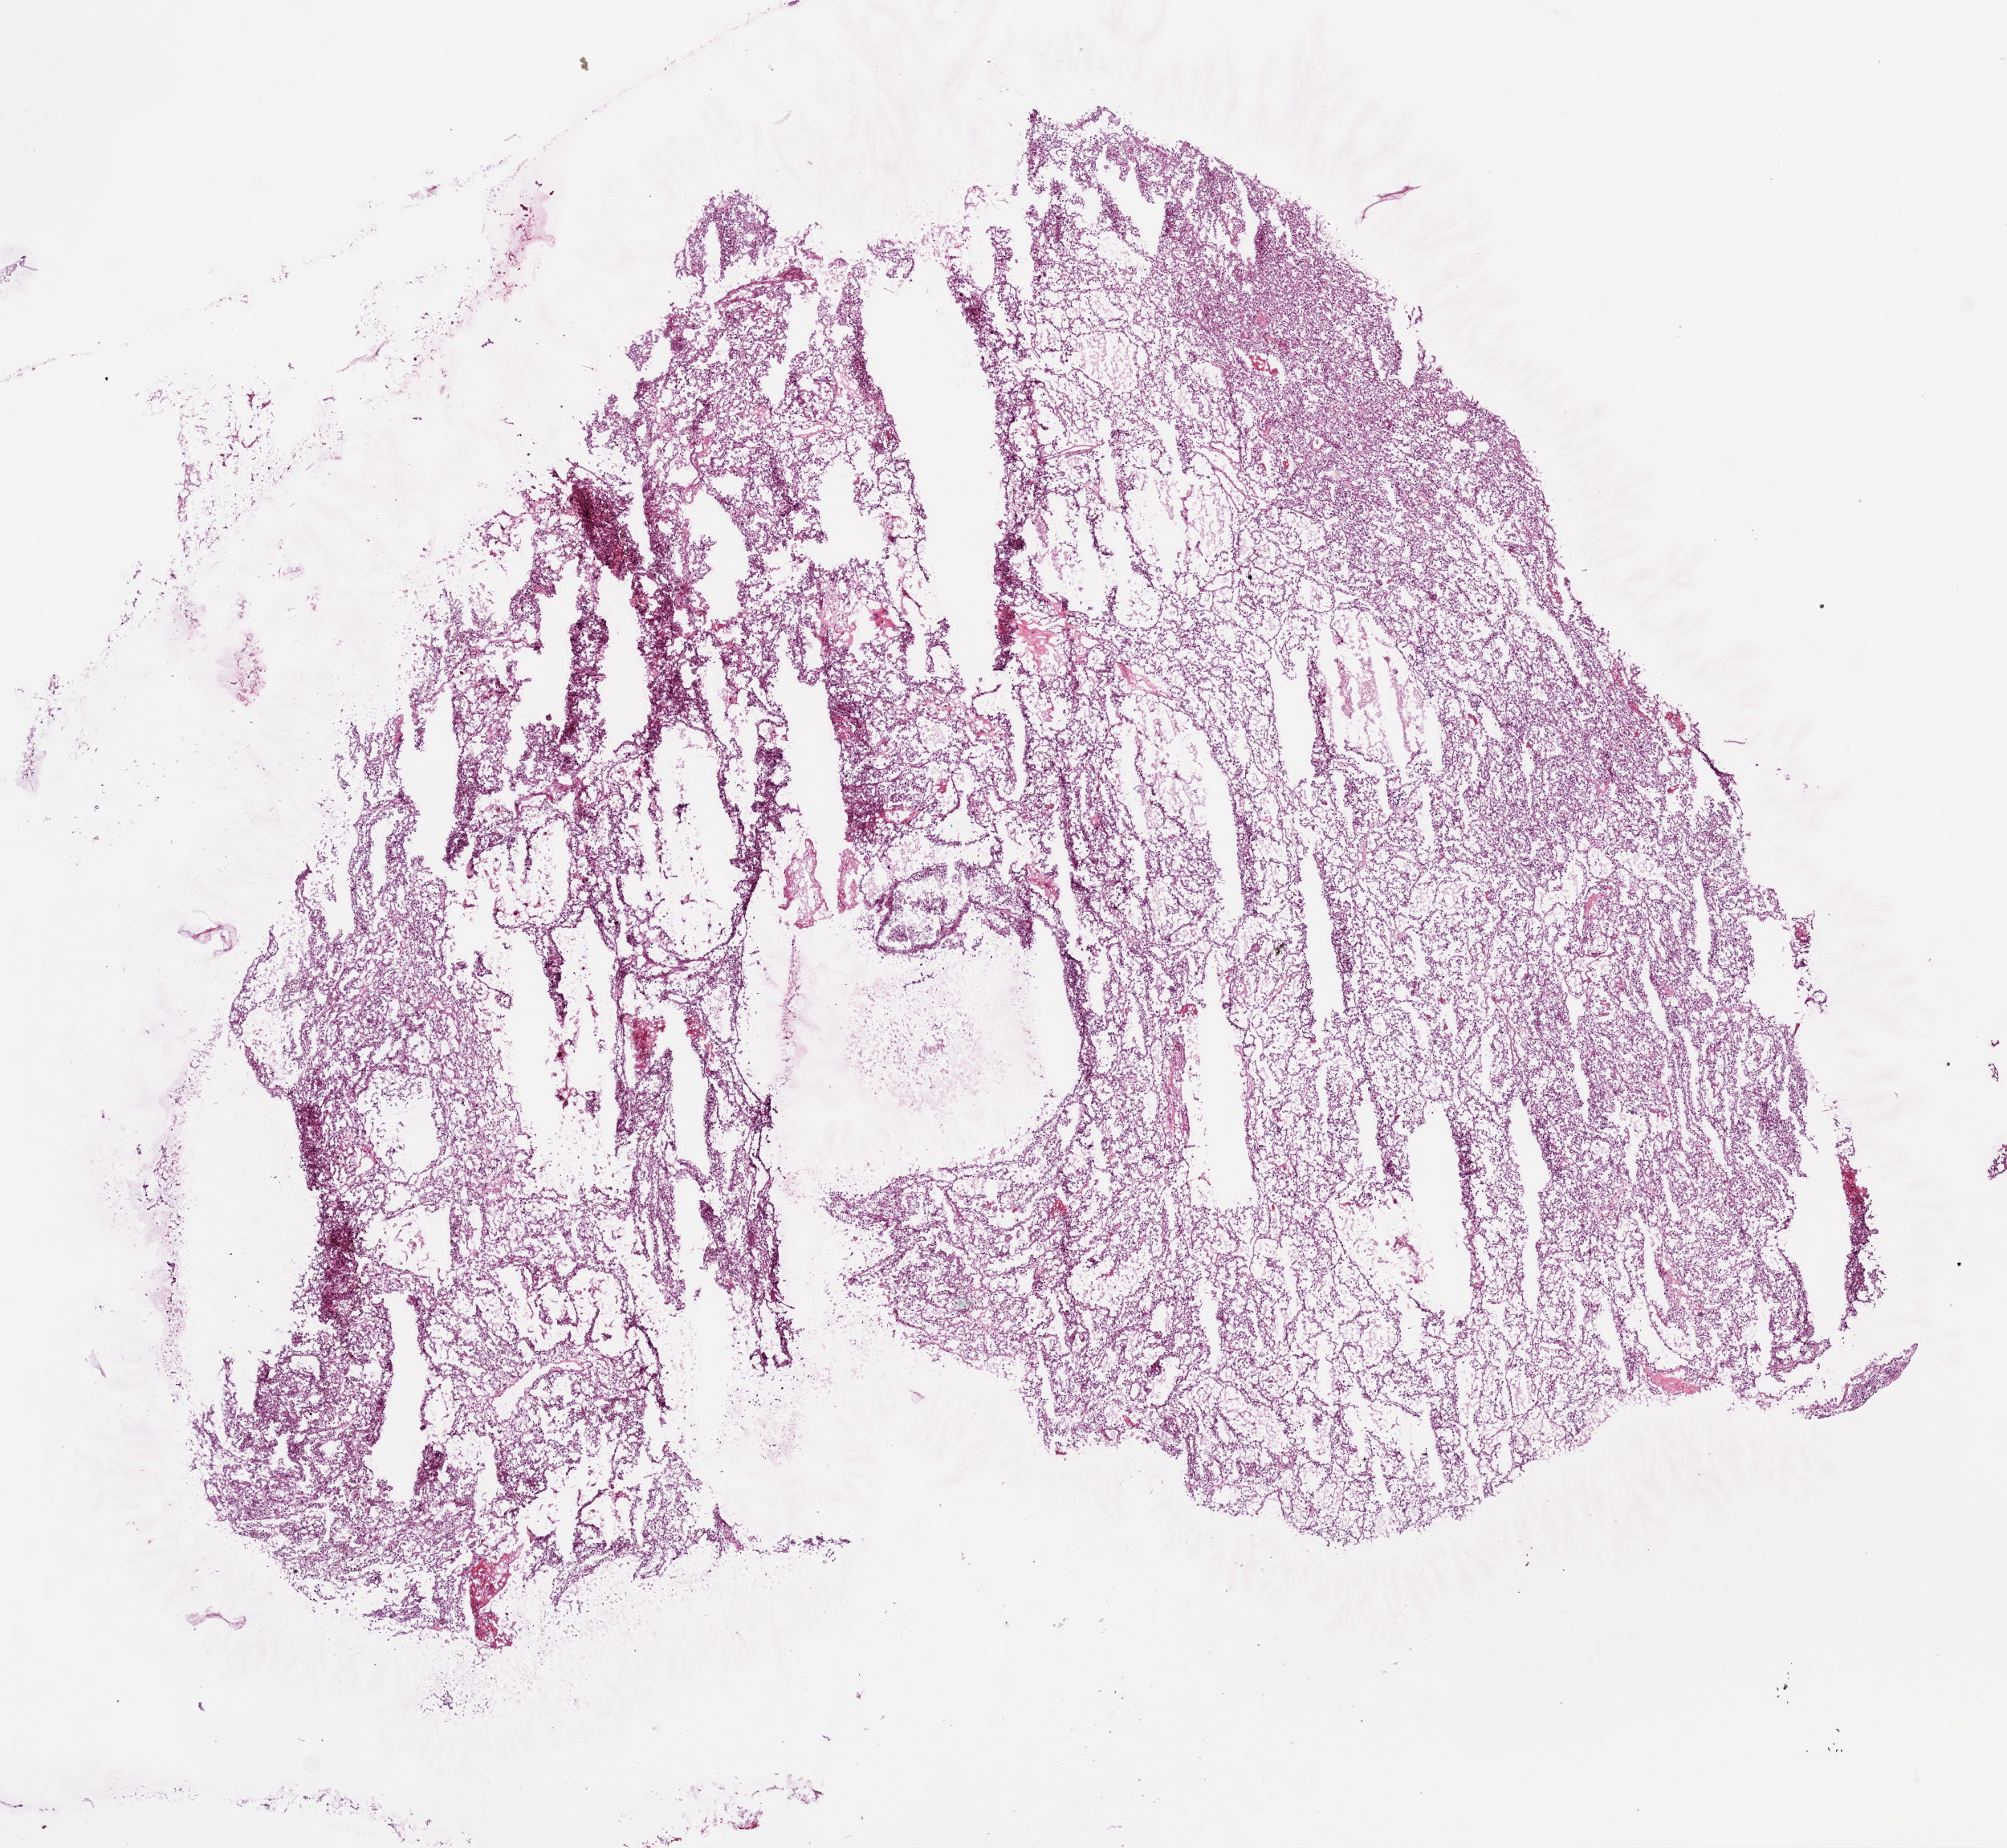
Digitized H&E-stained tissue section (whole slide), whole scanned area (about 10.0 x 9.2 mm, acquisition: 20x scan) shown as a low-resolution overview; frozen section; sample: primary tumour, kidney. Patient: male, age at initial diagnosis 77 years. Histologic grade: G3 (poorly differentiated). Slide review estimates, as recorded: tumour cells 90%, tumour nuclei 80%, normal cells 0%, stromal cells 10%, necrosis 0%.
* TNM: T1a N0 M0
* AJCC pathologic stage: I
* diagnosis: Clear cell adenocarcinoma, NOS